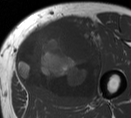
MRI of an extremity soft-tissue mass, one axial slice. Position 31 of 55 along the scan axis. MR volume resampled by the dataset authors to the PET/CT grid (not the native acquisition matrix). 3.27 mm slice thickness. 131 × 118 image matrix, field of view 128 × 115 mm. Male patient. From the clinical record (not read from this slice): histological type: pleiomorphic liposarcoma; grade: high; site of the primary tumour: left thigh.
Outlined on this slice (expert contour drawn on MRI and transferred to this co-registered scan by the dataset authors):
- gross tumour volume including surrounding oedema: bounding box (x1, y1, x2, y2) in pixels: (14, 18, 108, 102)
- gross tumour volume (mass): (14, 18, 104, 102)